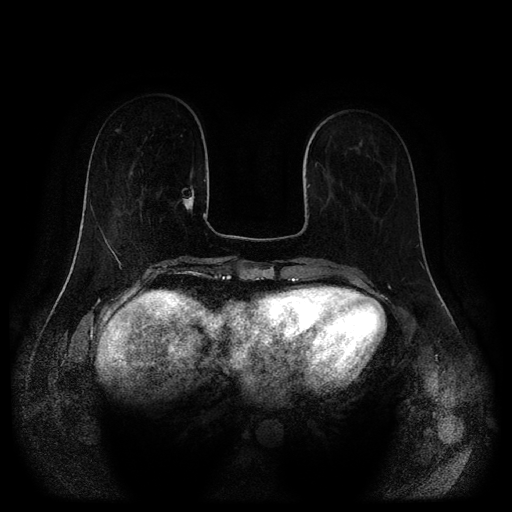
Breast MRI (dynamic contrast-enhanced, multi-phase), one axial slice. Position 36 of 116 along the scan axis. Dynamic contrast-enhanced series, time point 2 of 5 at this slice position (early post-contrast). 1.5 T. TE 2.6 ms, TR 5.2 ms. 2 mm slice thickness. 512 × 512 image matrix, field of view 380 × 380 mm. Patient: female, 62 years.
Outlined on this slice (semi-automatically segmented with operator editing):
- breast lesion (labelled 'tumour' in the annotation; benign lesions carry a separate 'benign' label): bounding box (x1, y1, x2, y2) in pixels: (177, 185, 195, 211)